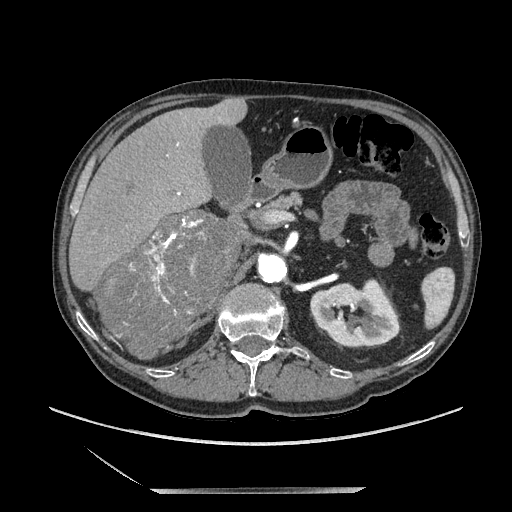
Contrast-enhanced abdominal CT, one axial slice. Position 119 of 243 along the scan axis. Soft-tissue window (W 400 / L 40 HU). 1.25 mm slice thickness. 512 × 512 image matrix, field of view 420 × 420 mm. Male patient. From the clinical record (not read from this slice): diagnosis: adrenocortical carcinoma; tumour side: right adrenal; tumour size at pathology: 16 cm; Ki-67 index: 17 %; stage (as recorded): 3.
Annotated regions visible in this slice (semi-automatically segmented with operator editing):
- mass: box from (x=102, y=211) to (x=234, y=357) px